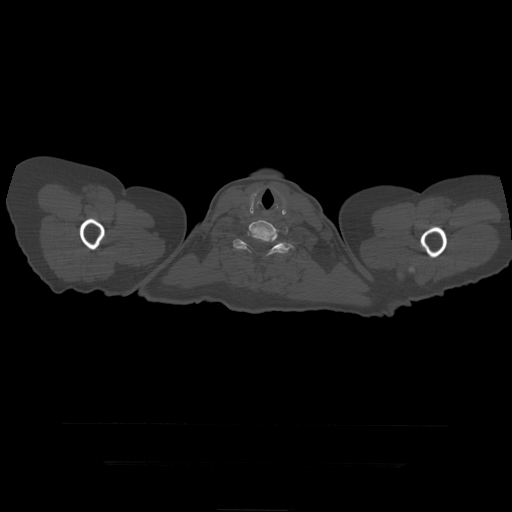
CT including the spine, one axial slice. Slice 394 of 399 in the series (ordered by position). Bone window (W 1800 / L 400 HU). 1.25 mm slice thickness. 512 × 512 image matrix, field of view 450 × 450 mm. Patient age 41 years. Case-level facts recorded for this patient, not image findings: primary cancer: breast.
Annotated regions visible in this slice (semi-automatically segmented with operator editing):
- T1 vertebra: box from (x=233, y=232) to (x=296, y=254) px